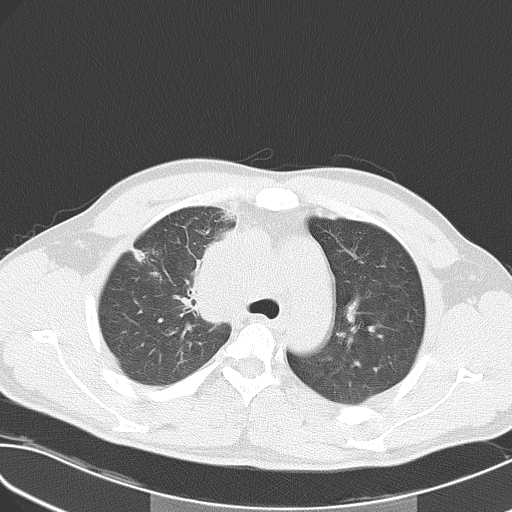
Chest CT, one axial slice; slice 40 of 55 in the series (ordered by position); reconstruction kernel B70f; 120 kVp; lung window (W 1500 / L -600 HU); 5 mm slice thickness; 512 × 512 image matrix, field of view 346 × 346 mm. Patient: male, 32 years. From the clinical record (not read from this slice): clinical TNM (as recorded): T4 N3 M0; histopathological grade: G3.
Annotated regions visible in this slice (bounding box drawn by a radiologist):
- lung tumour (recorded histology: small cell carcinoma): bounding box [x1, y1, x2, y2] px = [189, 222, 240, 324]